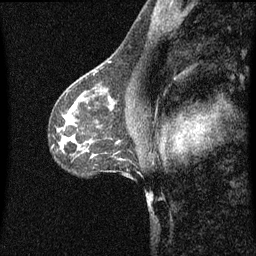
Breast MRI (dynamic contrast-enhanced), one sagittal slice. Dynamic contrast-enhanced series, image 2 of 3 at this slice position (ordered by acquisition). 1.5 T. TE 4.2 ms, TR 8.4 ms. 2 mm slice thickness. 256 × 256 image matrix, field of view 200 × 200 mm. Patient: female, 41 years.
Outlined on this slice (semi-automatically segmented with operator editing):
- analysis volume of interest (the breast-tissue region the enhancement analysis was run in; not a lesion): bounding box [x1, y1, x2, y2] px = [94, 72, 119, 97]
- tumour enhancement mask (voxels above the 70 % enhancement threshold inside the analysis volume of interest): [98, 84, 101, 87]